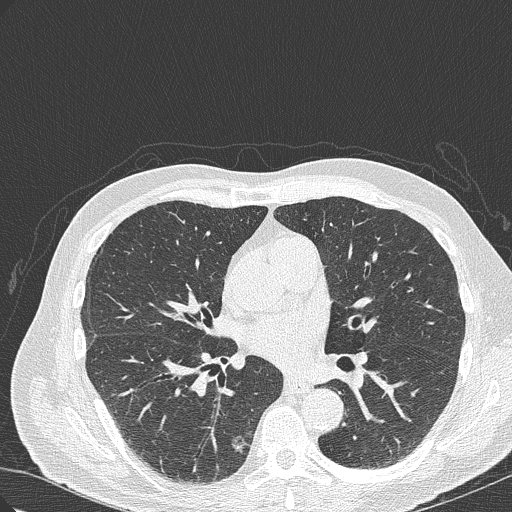
Chest CT (low-dose screening protocol), one axial image. Baseline screening round. Lung window (W 1500 / L -600 HU). Lung (sharp) reconstruction kernel (B50f). 512 × 512 image matrix. Male, age 70 years at enrolment. Current smoker at enrolment.
• Lesion marked by an expert reader, box from (x=197, y=420) to (x=260, y=482) px.
• The screening reader recorded 4 non-calcified nodules or masses ≥4 mm on this exam (right lower lobe, right lower lobe, right upper lobe, right lower lobe); which of them this box marks is not recorded.
• Official screen result: positive, change unspecified: nodule(s) >= 4 mm or enlarging nodule(s), mass(es), or other non-specific abnormalities suspicious for lung cancer.
• Participant outcome: lung cancer diagnosed 978 days after this screen — bronchiolo-alveolar adenocarcinoma, NOS, right lower lobe, poorly differentiated (G3), stage IB (AJCC 6th edition), 30 mm at pathology.